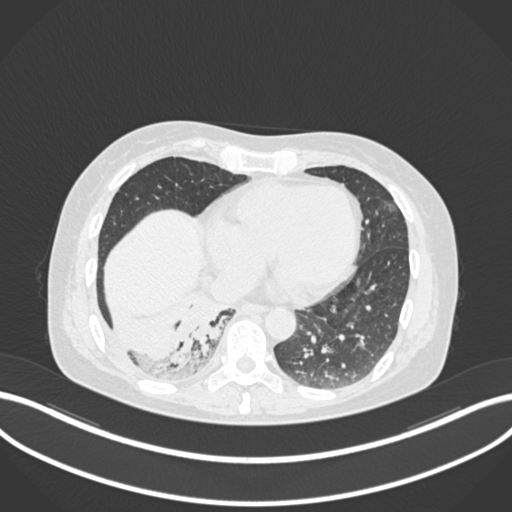
Chest CT, one axial slice; slice 43 of 168 in the series (ordered by position); reconstruction kernel B30f; 120 kVp; lung window (W 1500 / L -600 HU); 1 mm slice thickness; 512 × 512 image matrix, field of view 400 × 400 mm. Female patient, age 63 years. From the clinical record (not read from this slice): clinical TNM (as recorded): T1c N0 M0.
Annotated regions visible in this slice (bounding box drawn by a radiologist):
- lung tumour (recorded histology: adenocarcinoma): bounding box [x1, y1, x2, y2] px = [173, 299, 230, 353]